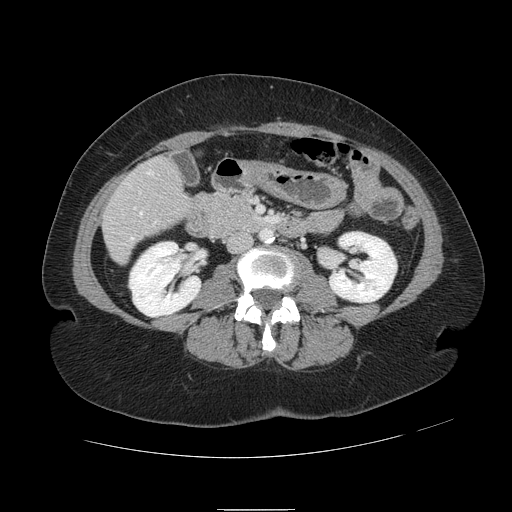
Contrast-enhanced abdominal CT, one axial slice. Position 23 of 121 along the scan axis. Soft-tissue window (W 400 / L 40 HU). 2.5 mm slice thickness. 512 × 512 image matrix. Female patient, age 52 years. Case-level facts recorded for this patient, not image findings: diagnosis: colorectal cancer liver metastases, imaged before liver resection; multiple liver metastases: yes; largest metastasis: 6.3 cm; chemotherapy before resection: yes.
Outlined on this slice (manually delineated by an expert):
- hepatic veins: bounding box (x1, y1, x2, y2) in pixels: (131, 171, 157, 240)
- liver: (104, 158, 186, 263)
- portal vein (with intrahepatic branches): (134, 207, 136, 209)